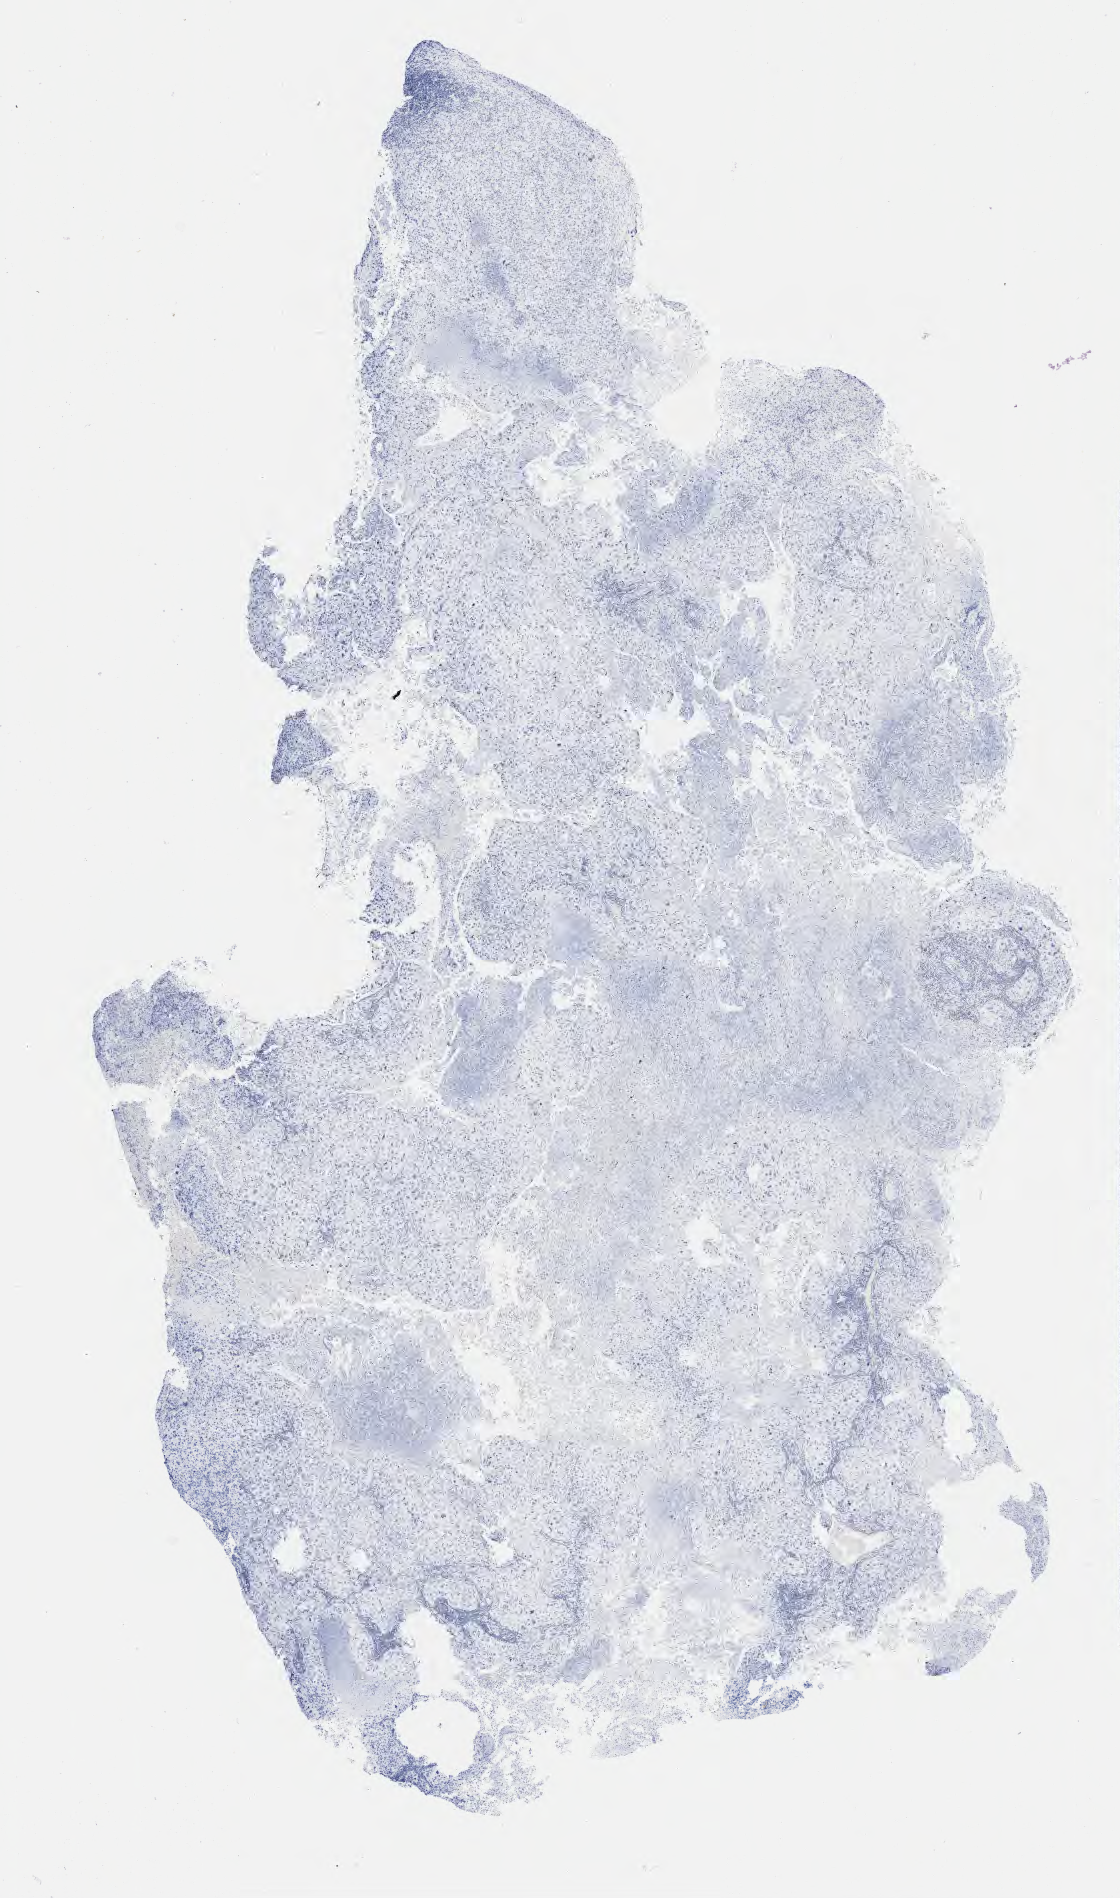
IHC for TTF-1 (thyroid transcription factor 1), whole-slide image — shown as a low-resolution overview of the whole scanned area (about 9.1 x 15.4 mm). Female patient.
Specimen: tumor tissue; site: lower respiratory tract.